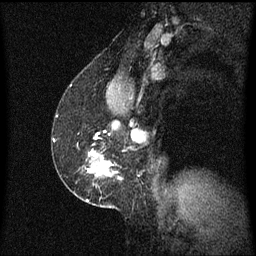
Breast MRI (dynamic contrast-enhanced), one sagittal slice. Position 38 of 60 along the scan axis. Dynamic contrast-enhanced series, image 2 of 3 at this slice position (ordered by acquisition). 1.5 T. TE 4.2 ms, TR 8.4 ms. 2 mm slice thickness. 256 × 256 image matrix, field of view 200 × 200 mm. Female patient, age 52 years. Case-level facts recorded for this patient, not image findings: setting: breast cancer imaged before/during neoadjuvant chemotherapy; receptor status: HER2-positive.
Outlined on this slice (semi-automatic segmentation, software-assisted and operator-edited):
- analysis volume of interest (the breast-tissue region the enhancement analysis was run in; not a lesion): bounding box [x1, y1, x2, y2] px = [62, 146, 121, 203]
- tumour enhancement mask (voxels above the 70 % enhancement threshold inside the analysis volume of interest): [89, 154, 121, 179]